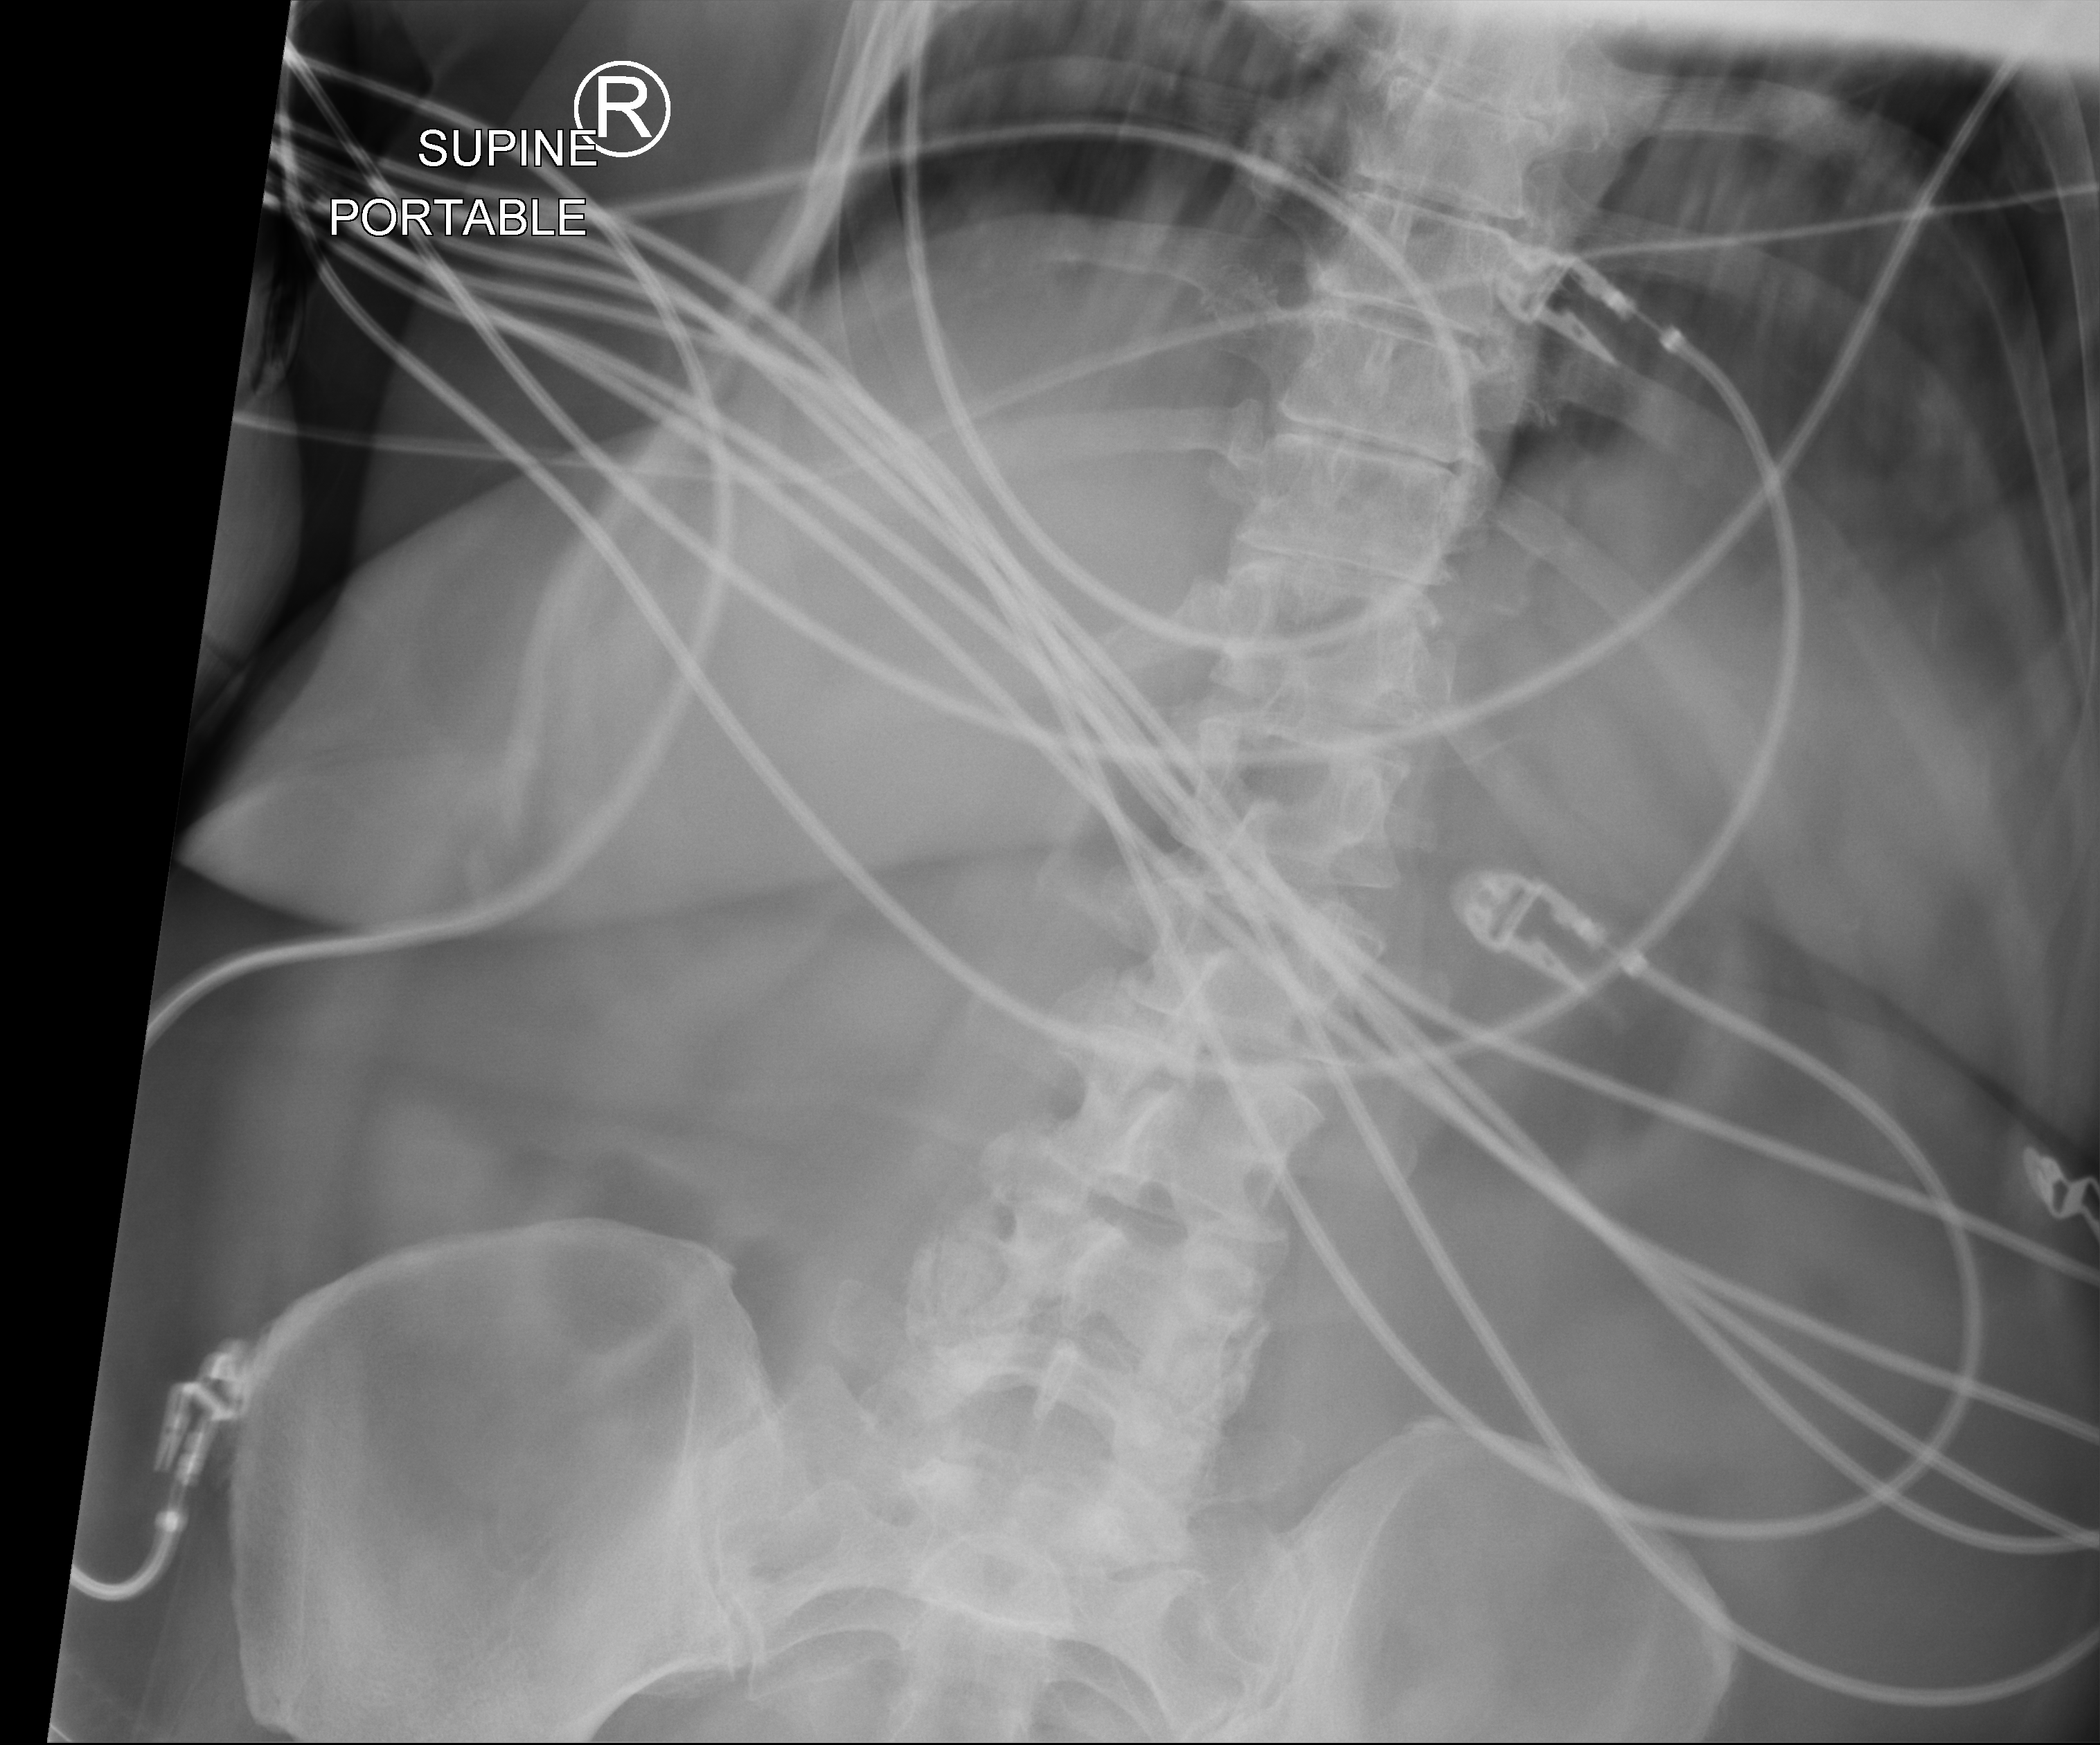
Bedside abdomen radiograph (computed radiography), anteroposterior (AP) projection. Patient hospitalised with COVID-19; female, aged 60–74 years.
Hospital-stay facts (about this admission, not read from this image; timing relative to this image not recorded):
- diabetes (admission record): no
- admitted to intensive care during this hospital stay: yes
- mechanically ventilated during this hospital stay: yes